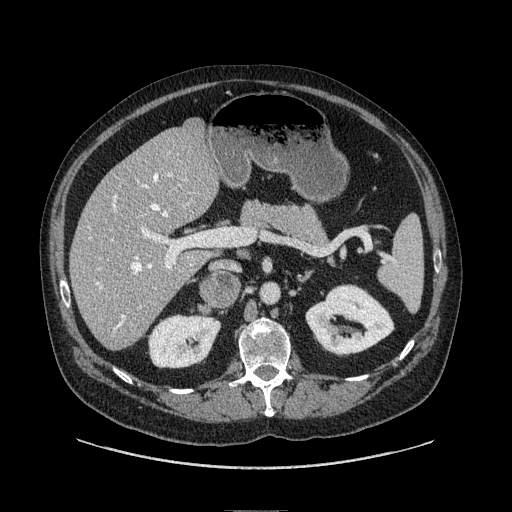
Contrast-enhanced abdominal CT, one axial slice; slice 42 of 149 in the series (ordered by position); soft-tissue window (W 400 / L 40 HU); 1.25 mm slice thickness; 512 × 512 image matrix. Male patient. Case-level facts recorded for this patient, not image findings: diagnosis: adrenocortical carcinoma; tumour side: right adrenal; tumour size at pathology: 7.5 cm; Ki-67 index: 15 %; stage (as recorded): 2.
Outlined on this slice (semi-automatic segmentation, software-assisted and operator-edited):
- mass: box from (x=201, y=274) to (x=240, y=308) px